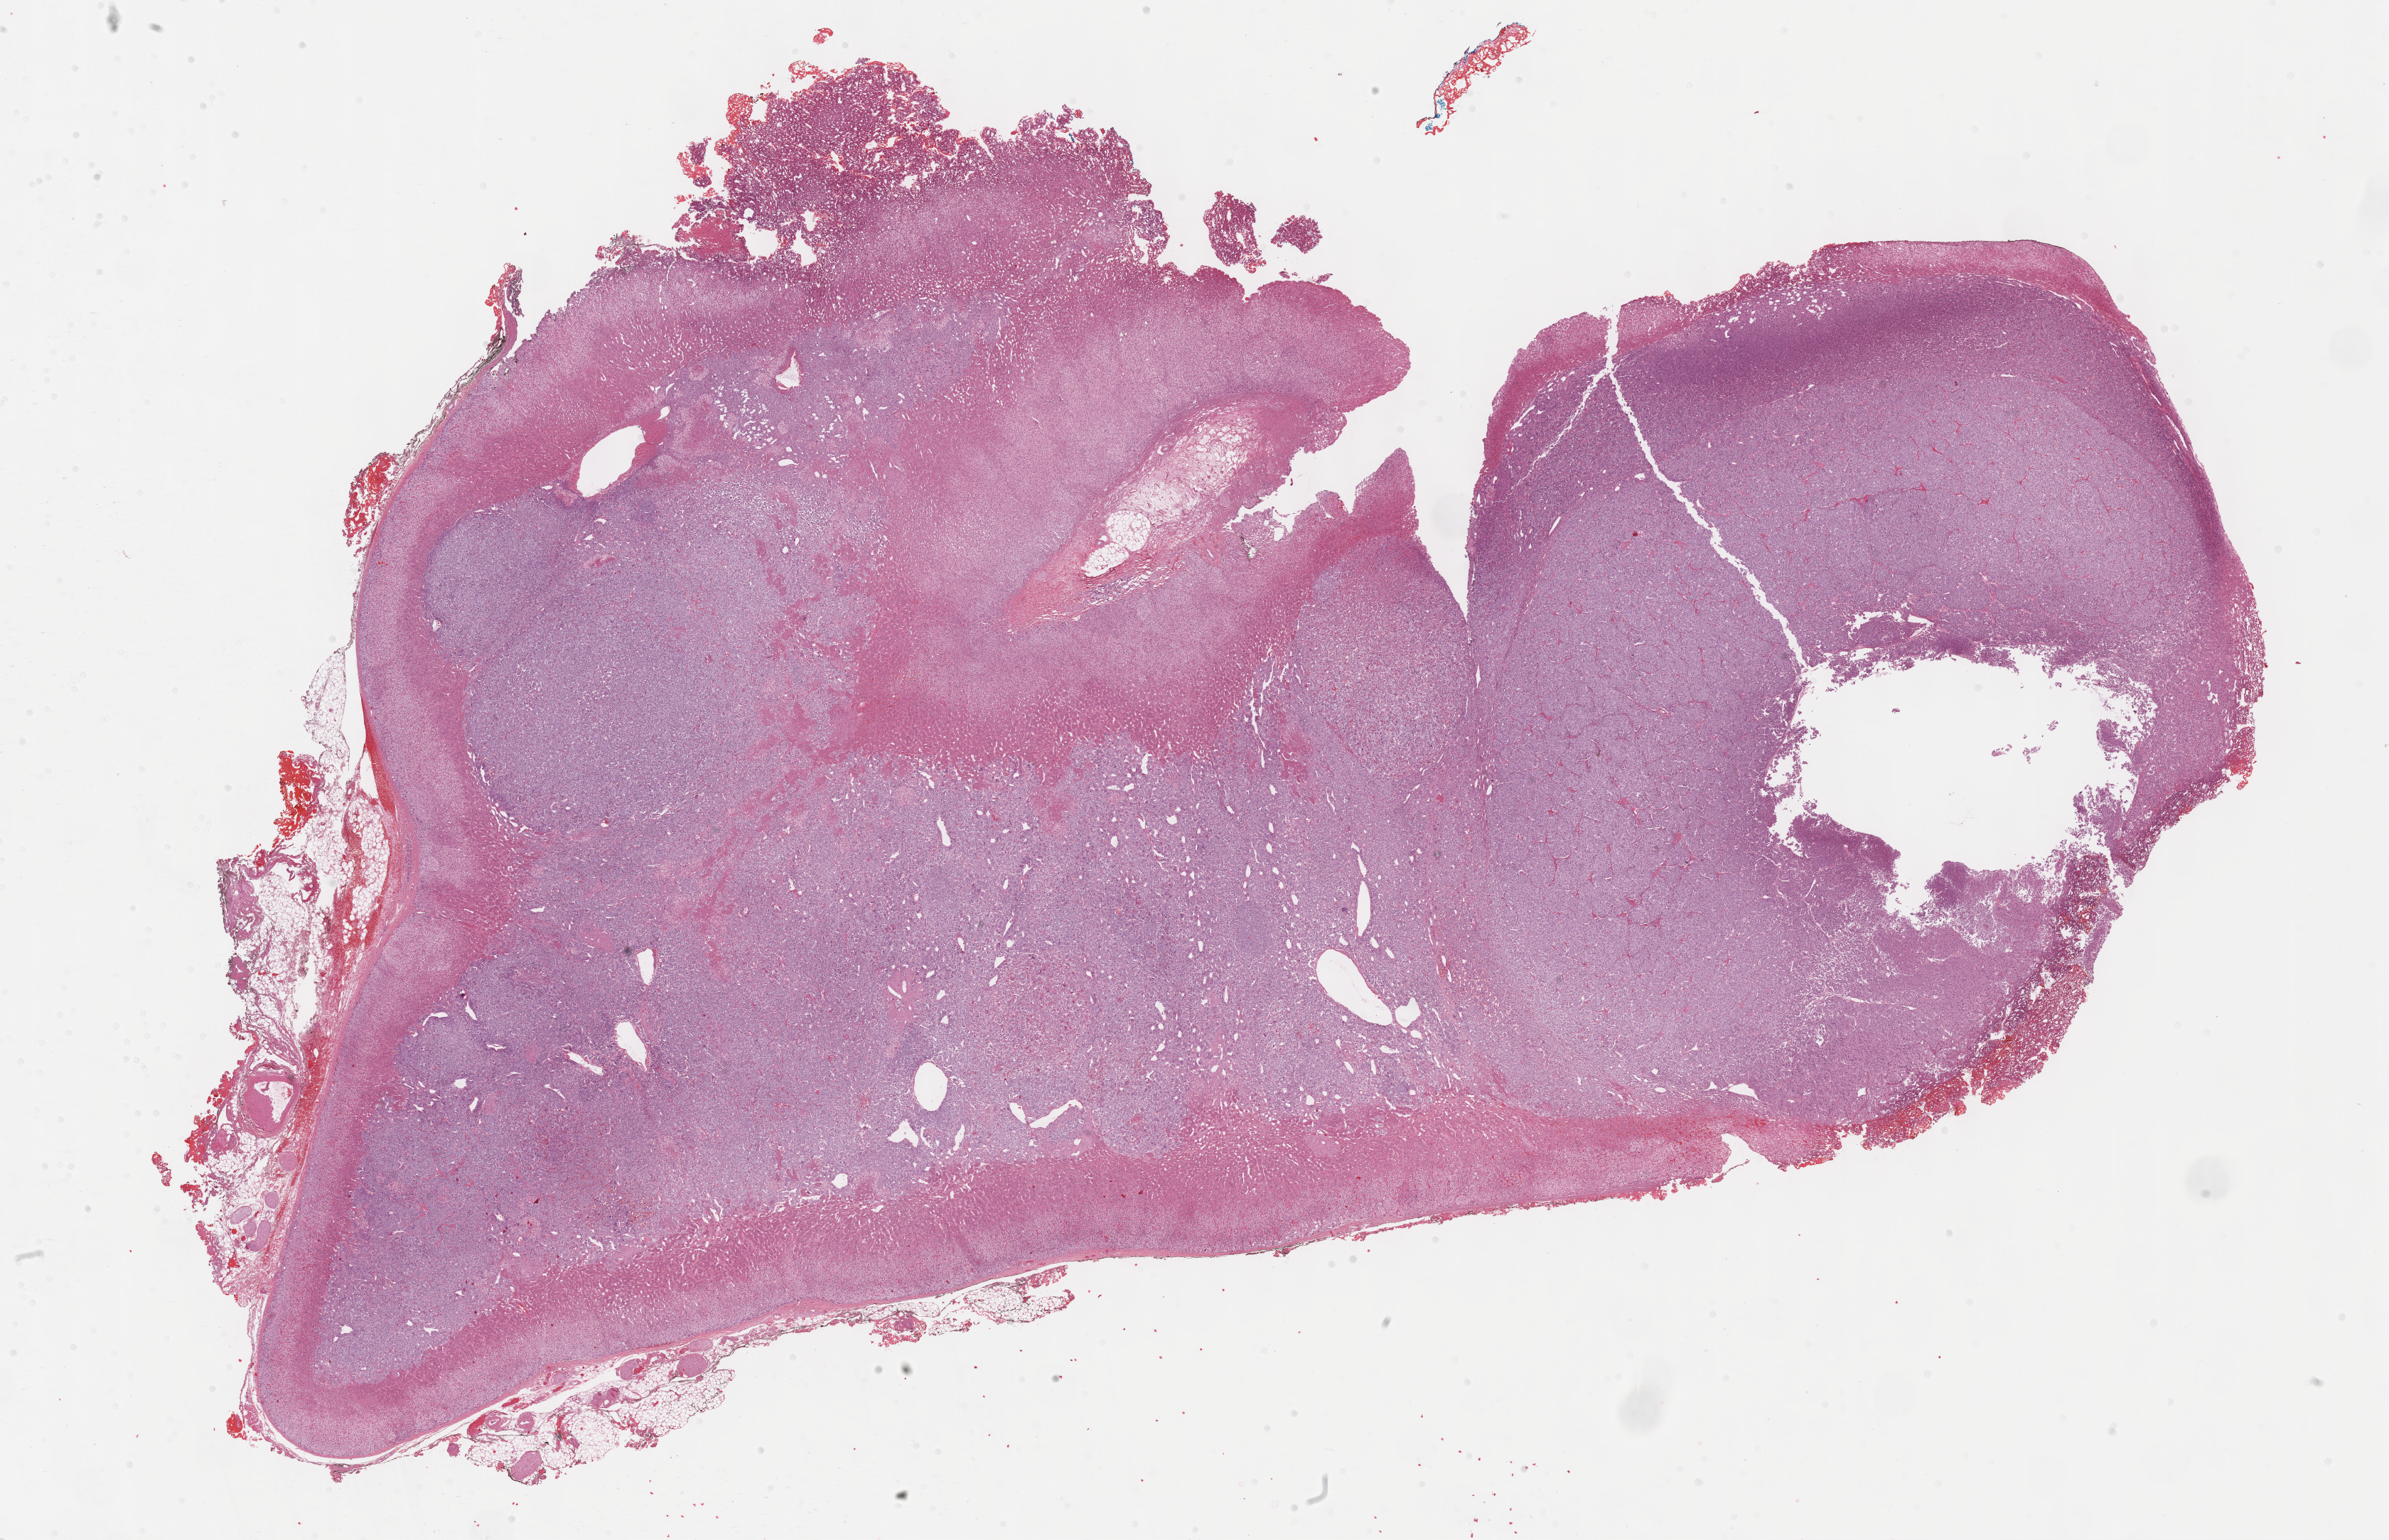
Whole-slide histology image, H&E — shown as a low-resolution overview of the whole scanned area (about 27.2 x 17.5 mm, from a 40x scan), formalin-fixed paraffin-embedded (FFPE) diagnostic section, primary tumour sample from the adrenal gland. Patient: male, age at initial diagnosis 24 years.
Histologic diagnosis: Medullary carcinoma, NOS (thyroid gland). Laterality: bilateral.